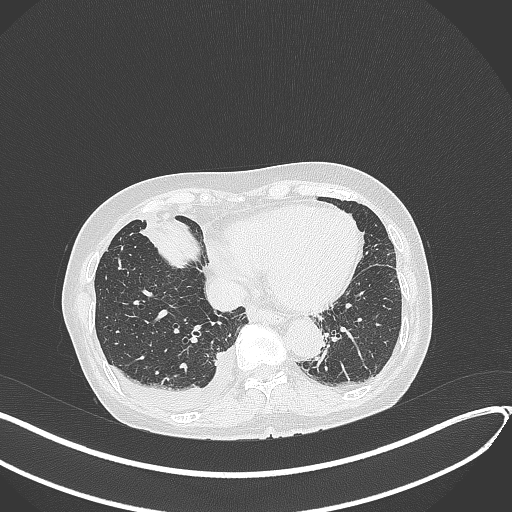
Chest CT, one axial slice. Slice 111 of 418 in the series (ordered by position). 120 kVp. Lung window (W 1500 / L -600 HU). 1 mm slice thickness. 512 × 512 image matrix, field of view 400 × 400 mm. Patient: female, 75 years. Case-level facts recorded for this patient, not image findings: clinical TNM (as recorded): T2a N3 M0.
Structures marked on this image (bounding box drawn by a radiologist):
- lung tumour (recorded histology: adenocarcinoma): bounding box <141,217,214,274> (left, top, right, bottom; pixels)